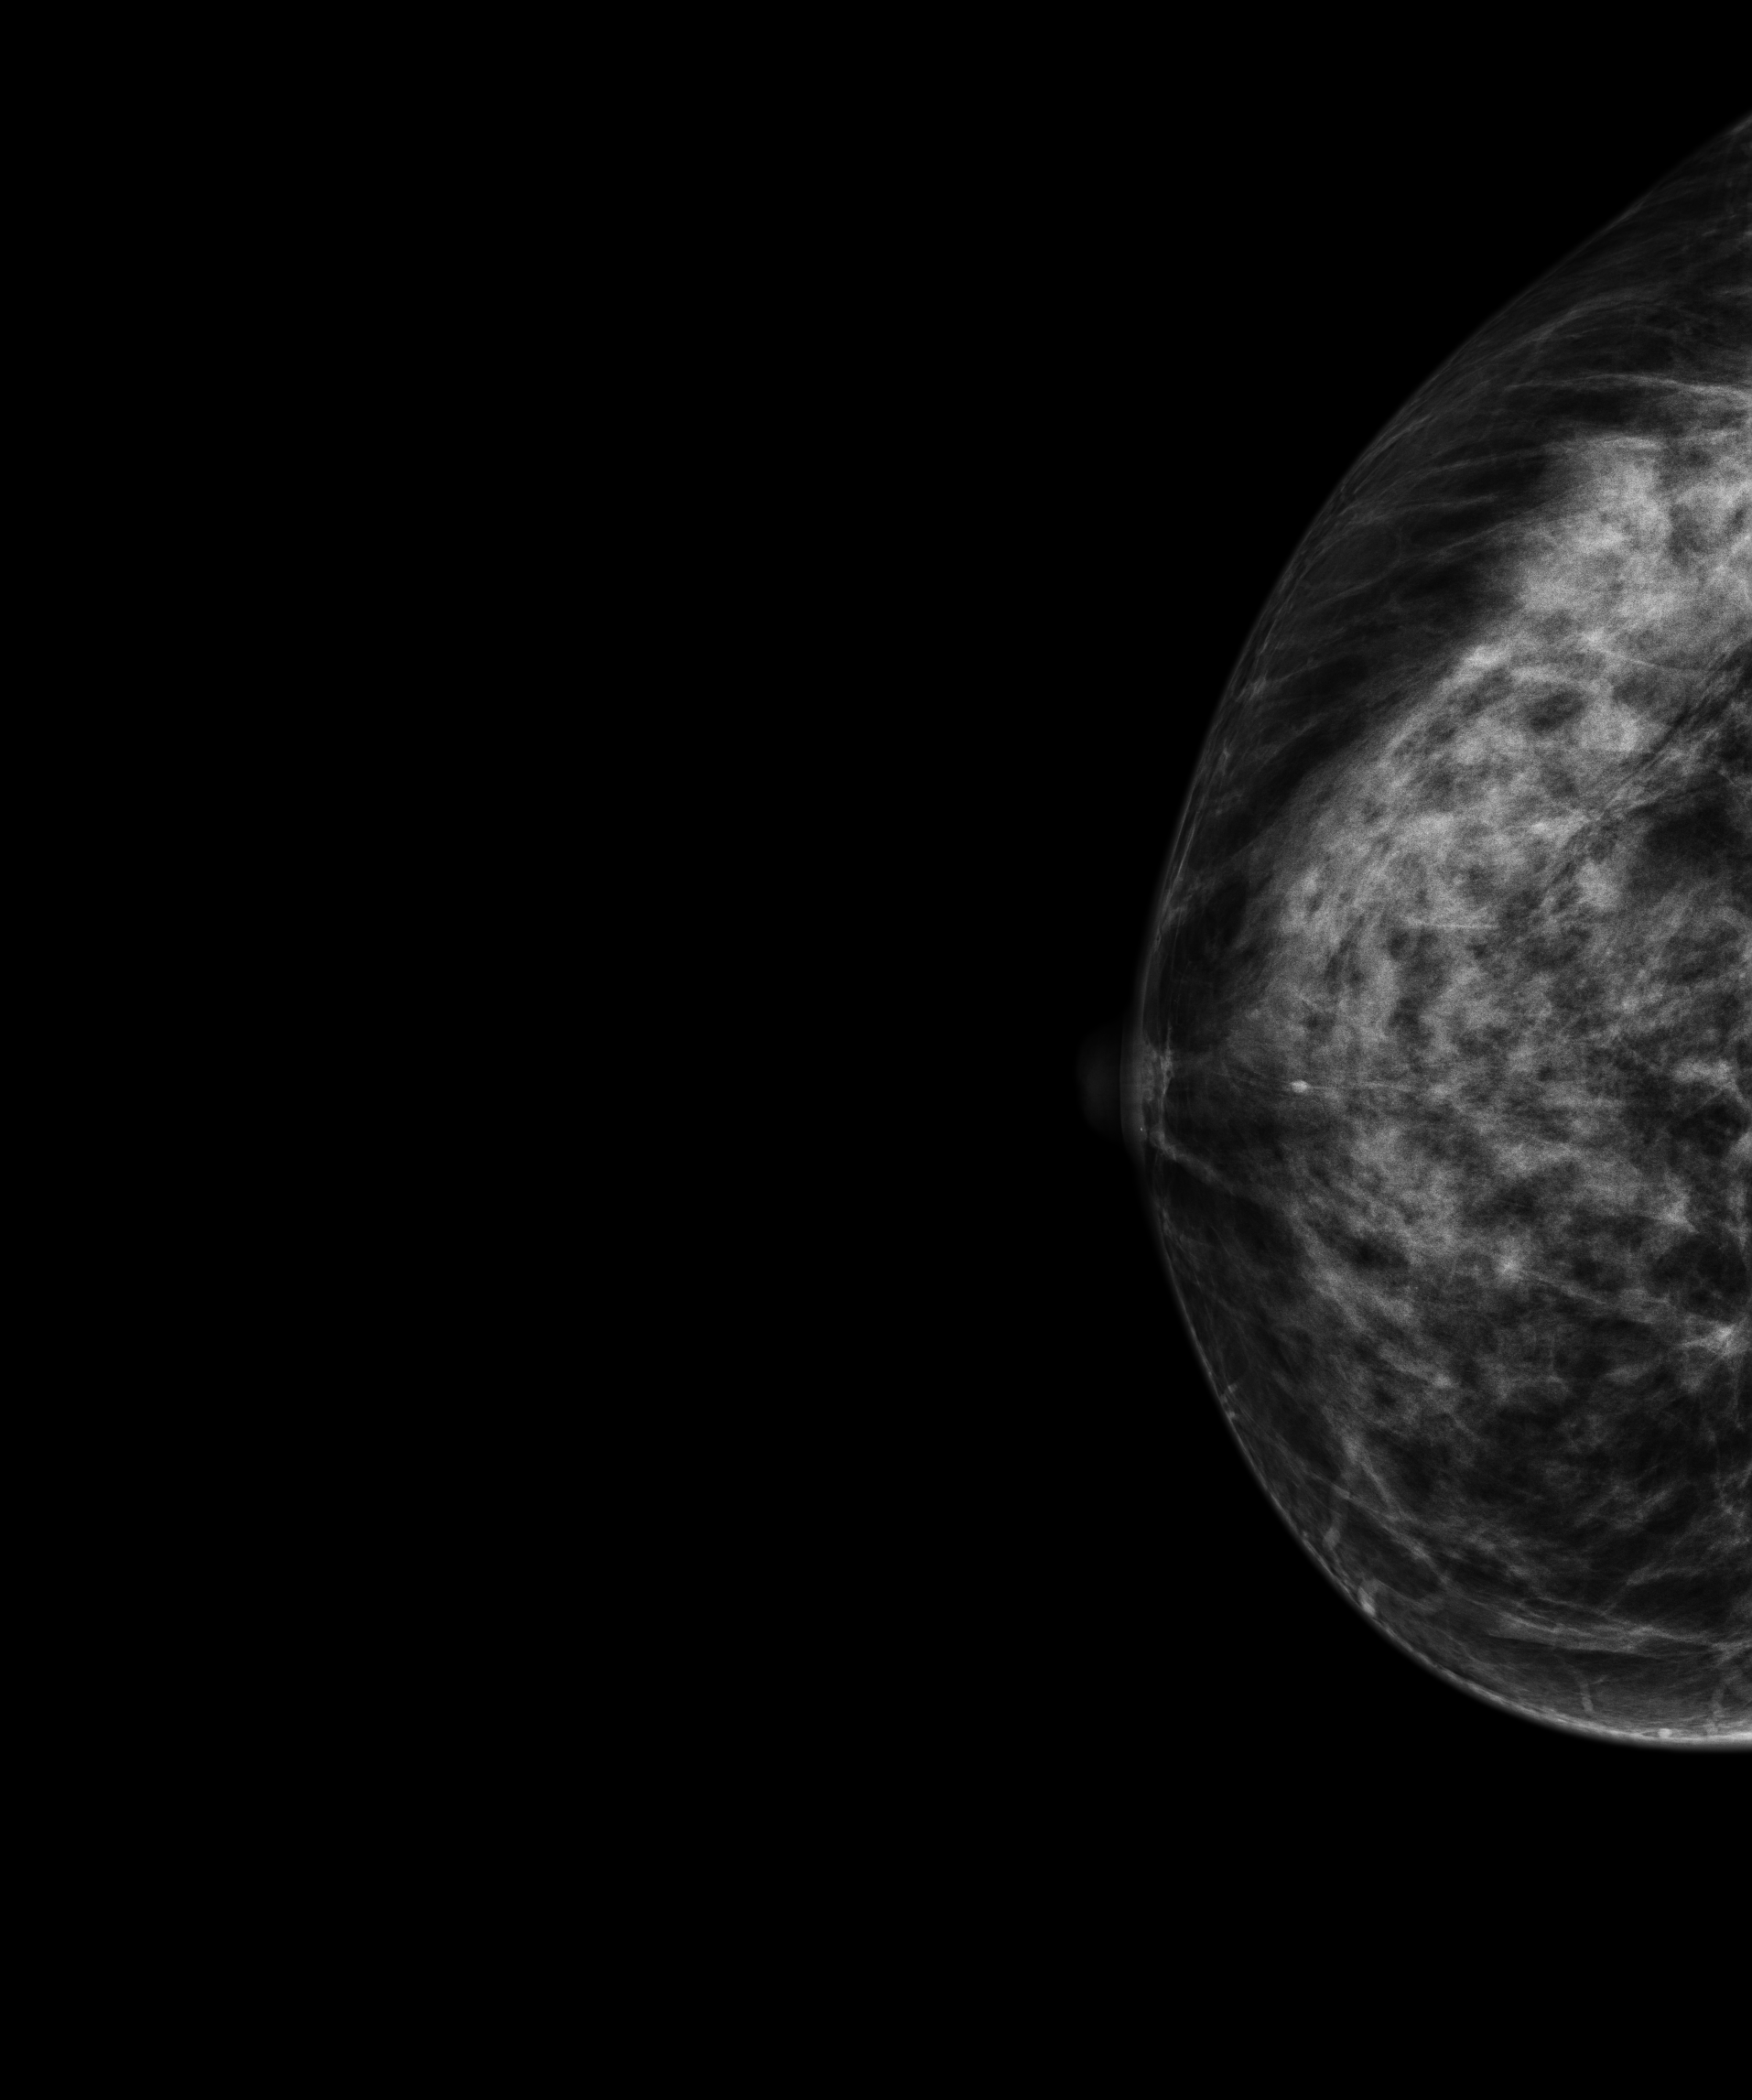
Full-field digital mammogram (FFDM), right breast, craniocaudal (CC) view, screening examination. Patient: female, 56 years.
Final BI-RADS assessment for this screening round (tomosynthesis exam, both breasts): category 1.